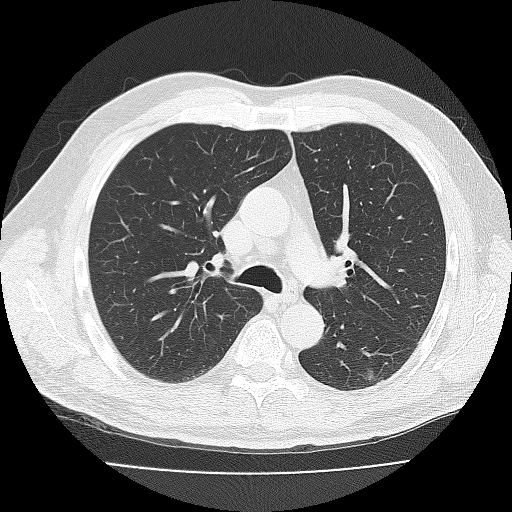
Low-dose screening chest CT, axial slice; second annual screen; lung window (W 1500 / L -600 HU); reconstruction kernel FC30 (as recorded); slice 35 of 96 in the series. Male participant, aged 65 years at enrolment. Former smoker at enrolment.
Expert reader's lesion annotation, bounding box (x1, y1, x2, y2) in pixels: (351, 355, 397, 398). Reader record for this screening exam (exam-level; its link to the box is not recorded): non-calcified nodule or mass ≥4 mm, left lower lobe, 11 × 10 mm, smooth margins, soft tissue attenuation, pre-existing on the prior screen: yes; interval growth: yes. Official screen result: positive, other. Later outcome: lung cancer diagnosed 8 days after this screen — adenocarcinoma, NOS, left lower lobe, well differentiated (G1), stage IB (AJCC 6th edition), 10 mm at pathology.